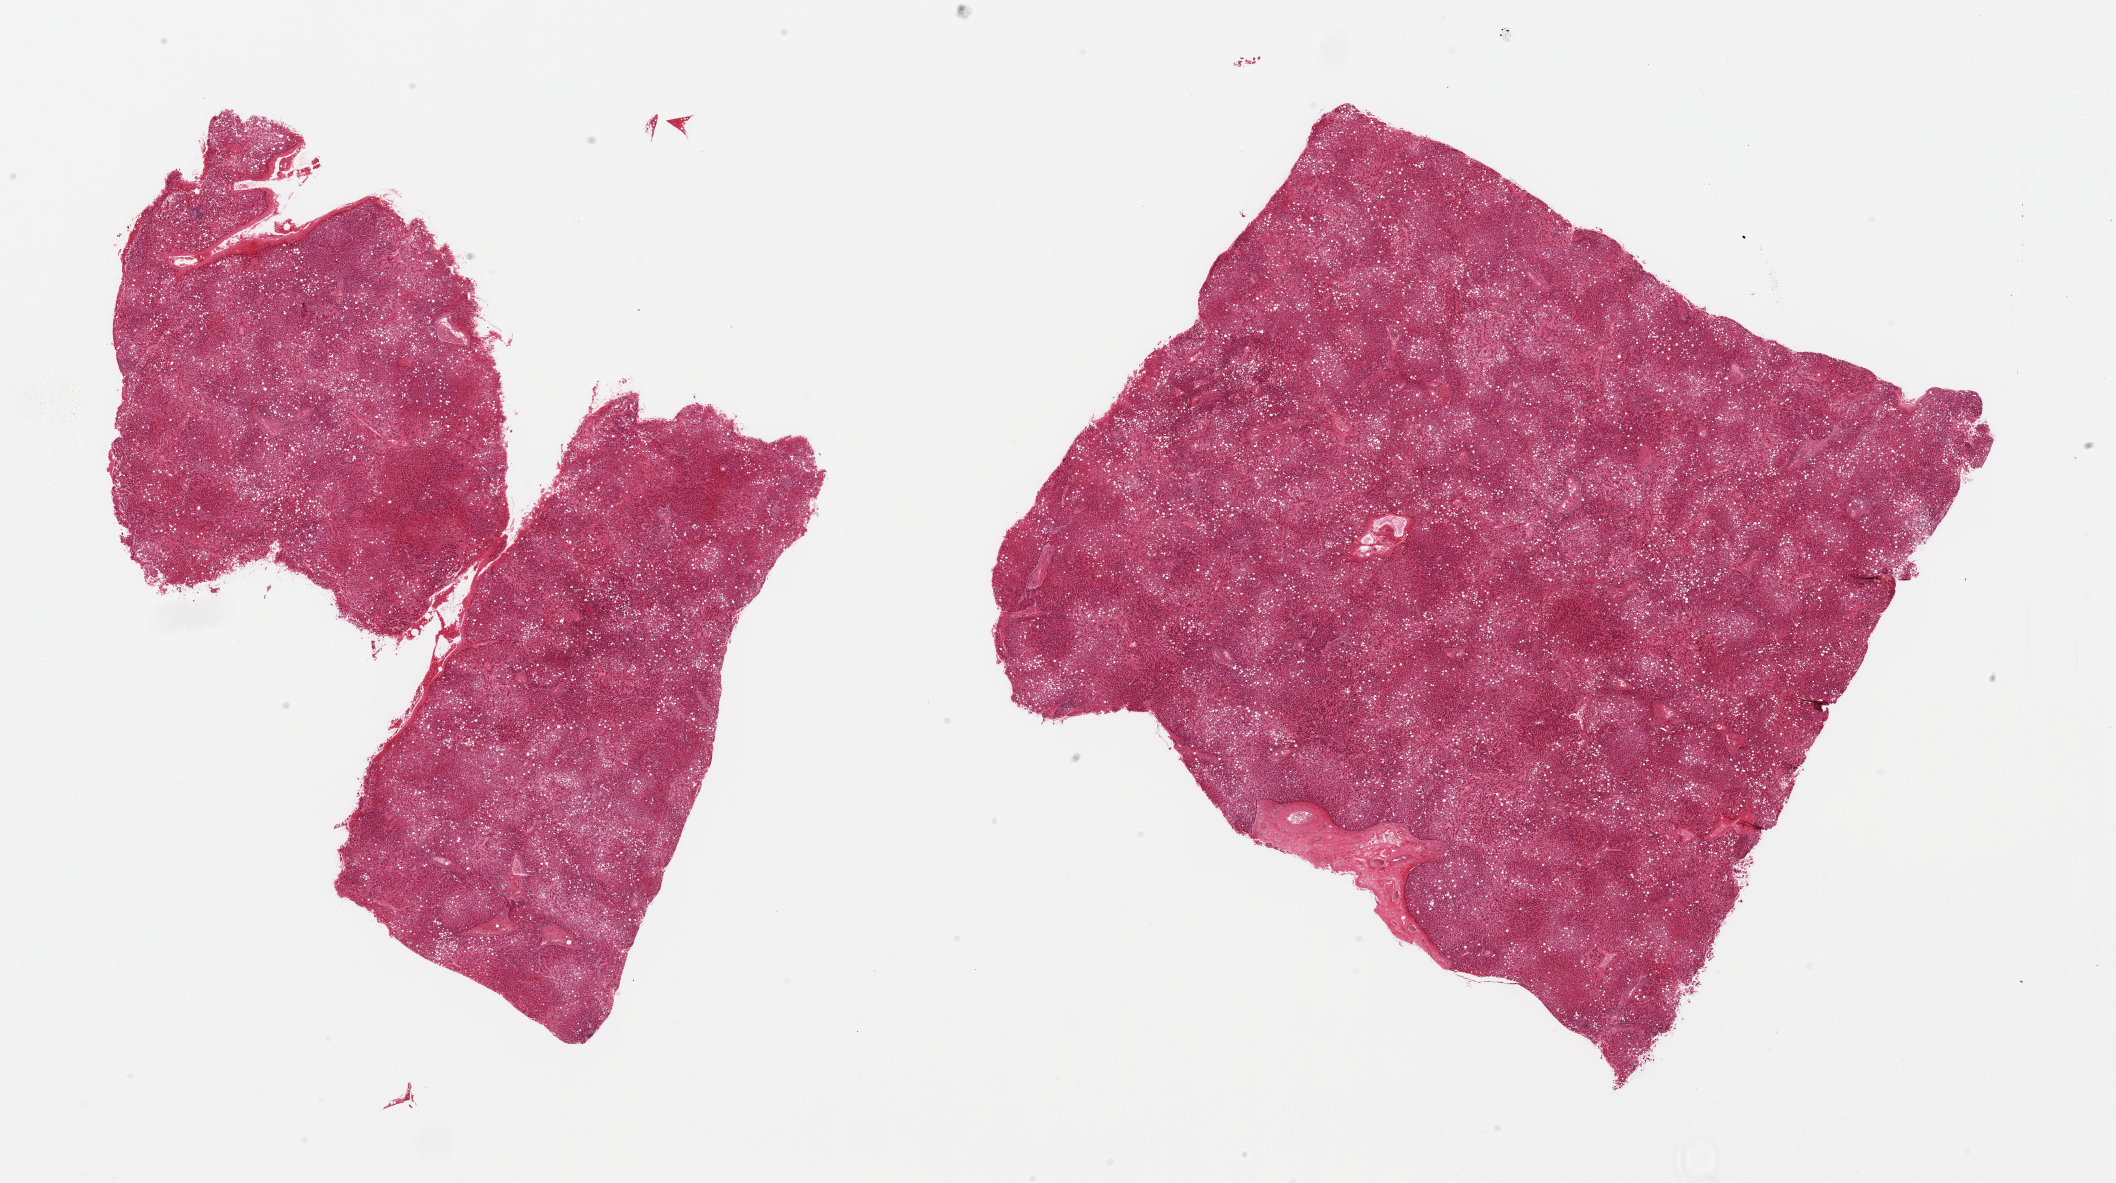
Digitized haematoxylin and eosin-stained section, brightfield — shown as a low-resolution overview of the whole scanned area (about 33.5 x 18.7 mm, slide scanned at 20x); PAXgene-fixed, paraffin-embedded tissue; sampled site (target tissue): liver; tissue donor sample. Male donor.
Pathologist's review note for this sample: 3 pieces; moderate macrovesicular steatosis.